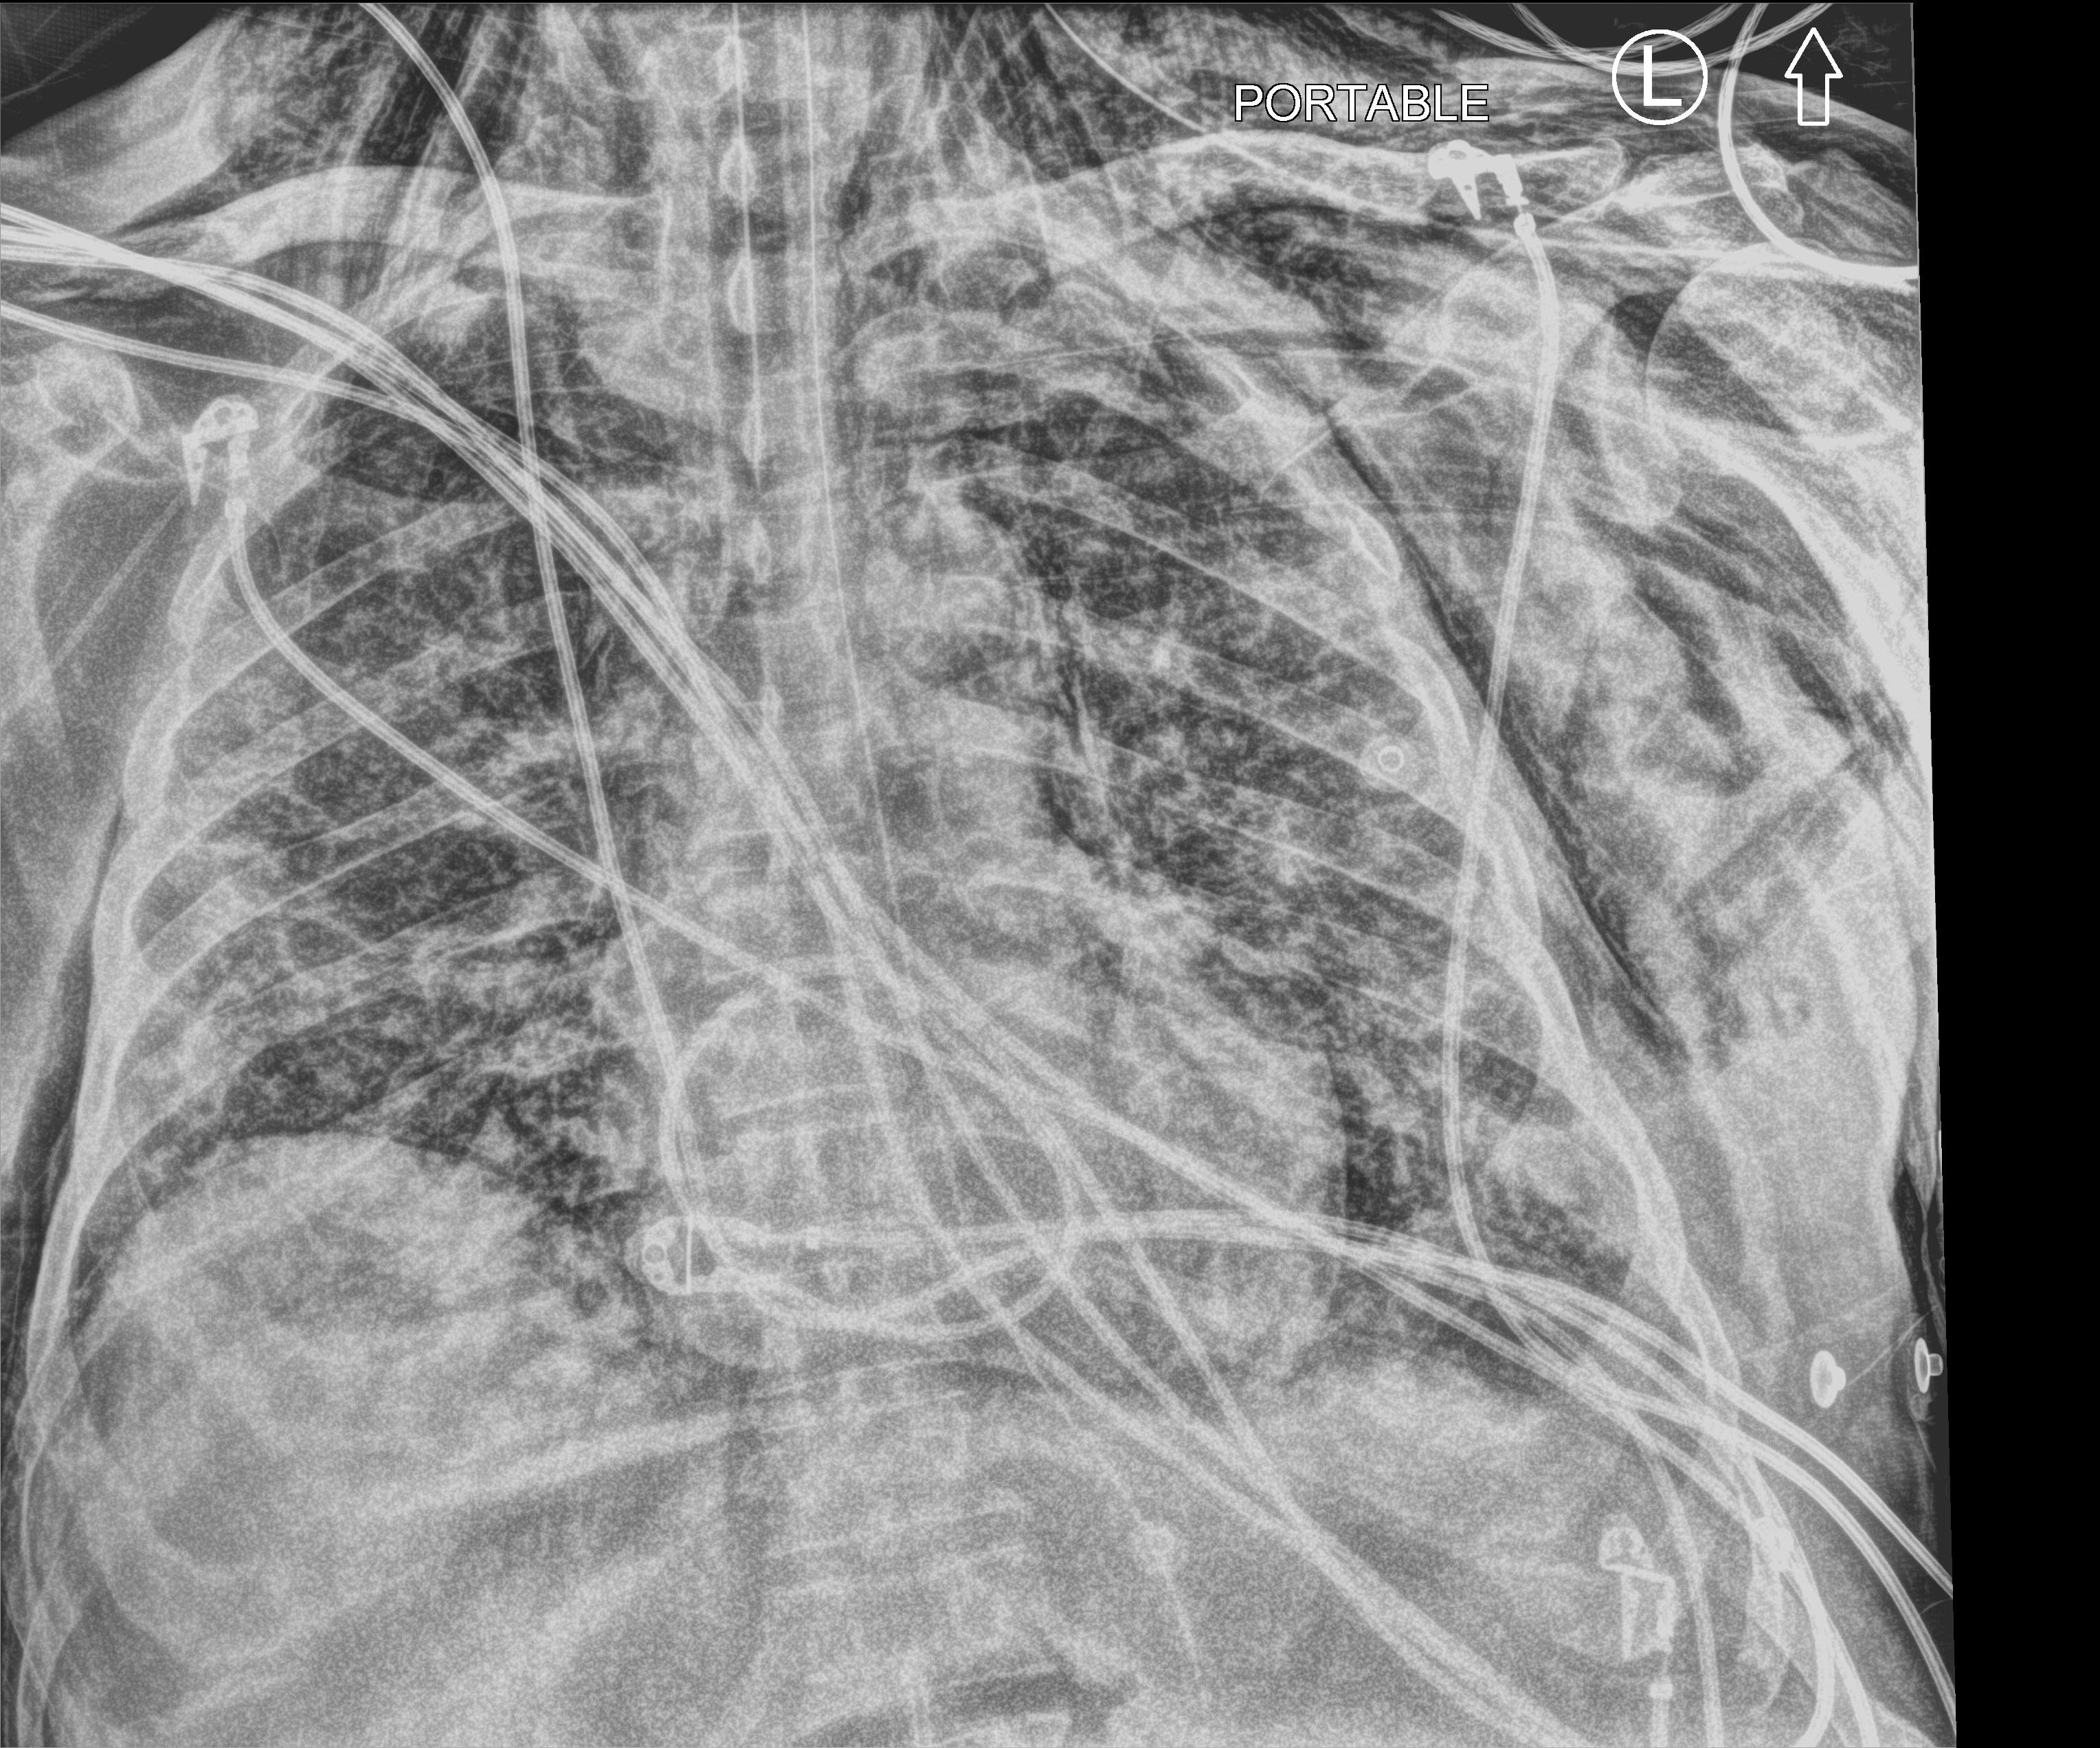
Chest X-ray (portable), anteroposterior (AP) projection. Male patient hospitalised with COVID-19, age 60–74 years.
Admission-level facts for this patient (not findings on this image; timing relative to this image not recorded): smoking status (admission record): former; mechanically ventilated during this hospital stay: yes; admitted to intensive care during this hospital stay: yes.